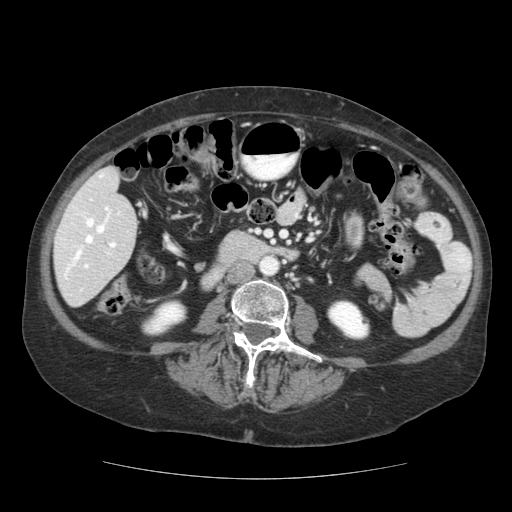
Contrast-enhanced abdominal CT (liver protocol), one axial slice. Slice 42 of 111 in the series (ordered by position). Reconstruction kernel STANDARD. 140 kVp. Soft-tissue window (W 400 / L 40 HU). 2.5 mm slice thickness. 512 × 512 image matrix, field of view 360 × 360 mm. Case-level facts recorded for this patient, not image findings: diagnosis: hepatocellular carcinoma (patient treated with transarterial chemoembolisation; whether this scan precedes or follows treatment is not stated here); TNM stage (as recorded): Stage-I; Child-Pugh class: A; tumour differentiation: moderately-poorly differentiated.
Annotated regions visible in this slice (semi-automatically segmented with operator editing):
- liver parenchyma outside the tumour (the mass and vessels are separate outlines, so this box may not span the whole liver): bounding box [x1, y1, x2, y2] px = [54, 166, 138, 306]
- liver vessels: [60, 173, 121, 291]